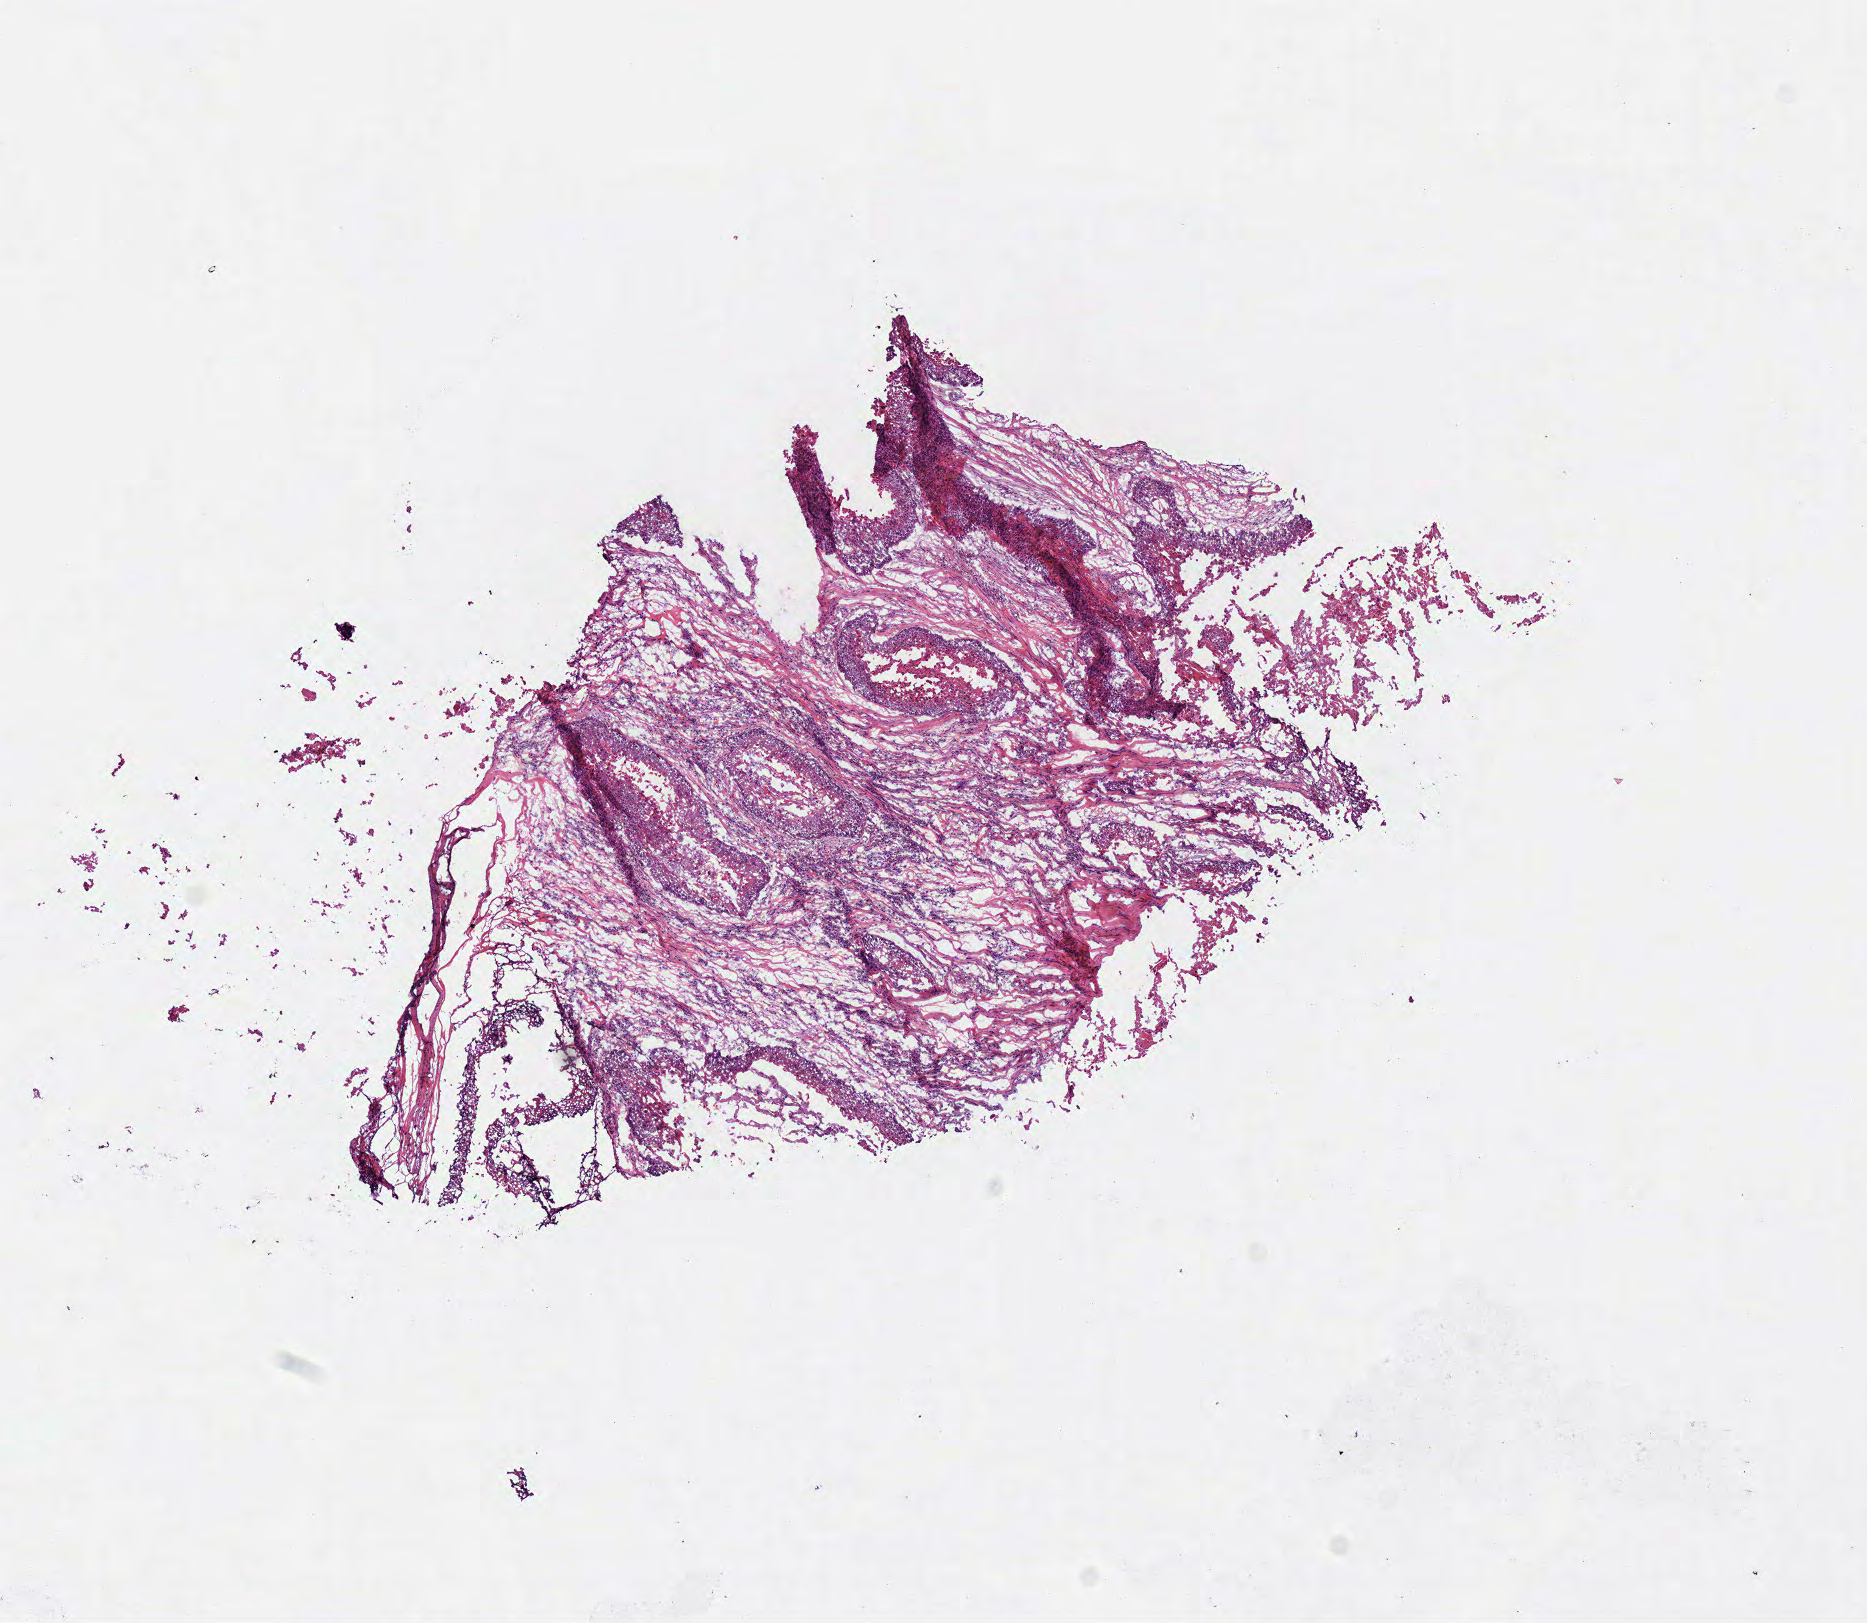
Digitized Hematoxylin and eosin (H&E) stained tissue section (whole slide), shown as a low-resolution overview of the whole scanned area (about 7.3 x 6.4 mm); frozen section; sample: primary tumour, head and neck. Patient: male, age at initial diagnosis 80 years. Histologic grade: G2 (moderately differentiated). Composition of this section per pathologist review: tumour cells 40%, tumour nuclei 50%, normal cells 0%, stromal cells 60%, necrosis 0%.
Diagnosis: Squamous cell carcinoma, NOS (larynx, NOS). AJCC pathologic stage: II (7th edition).